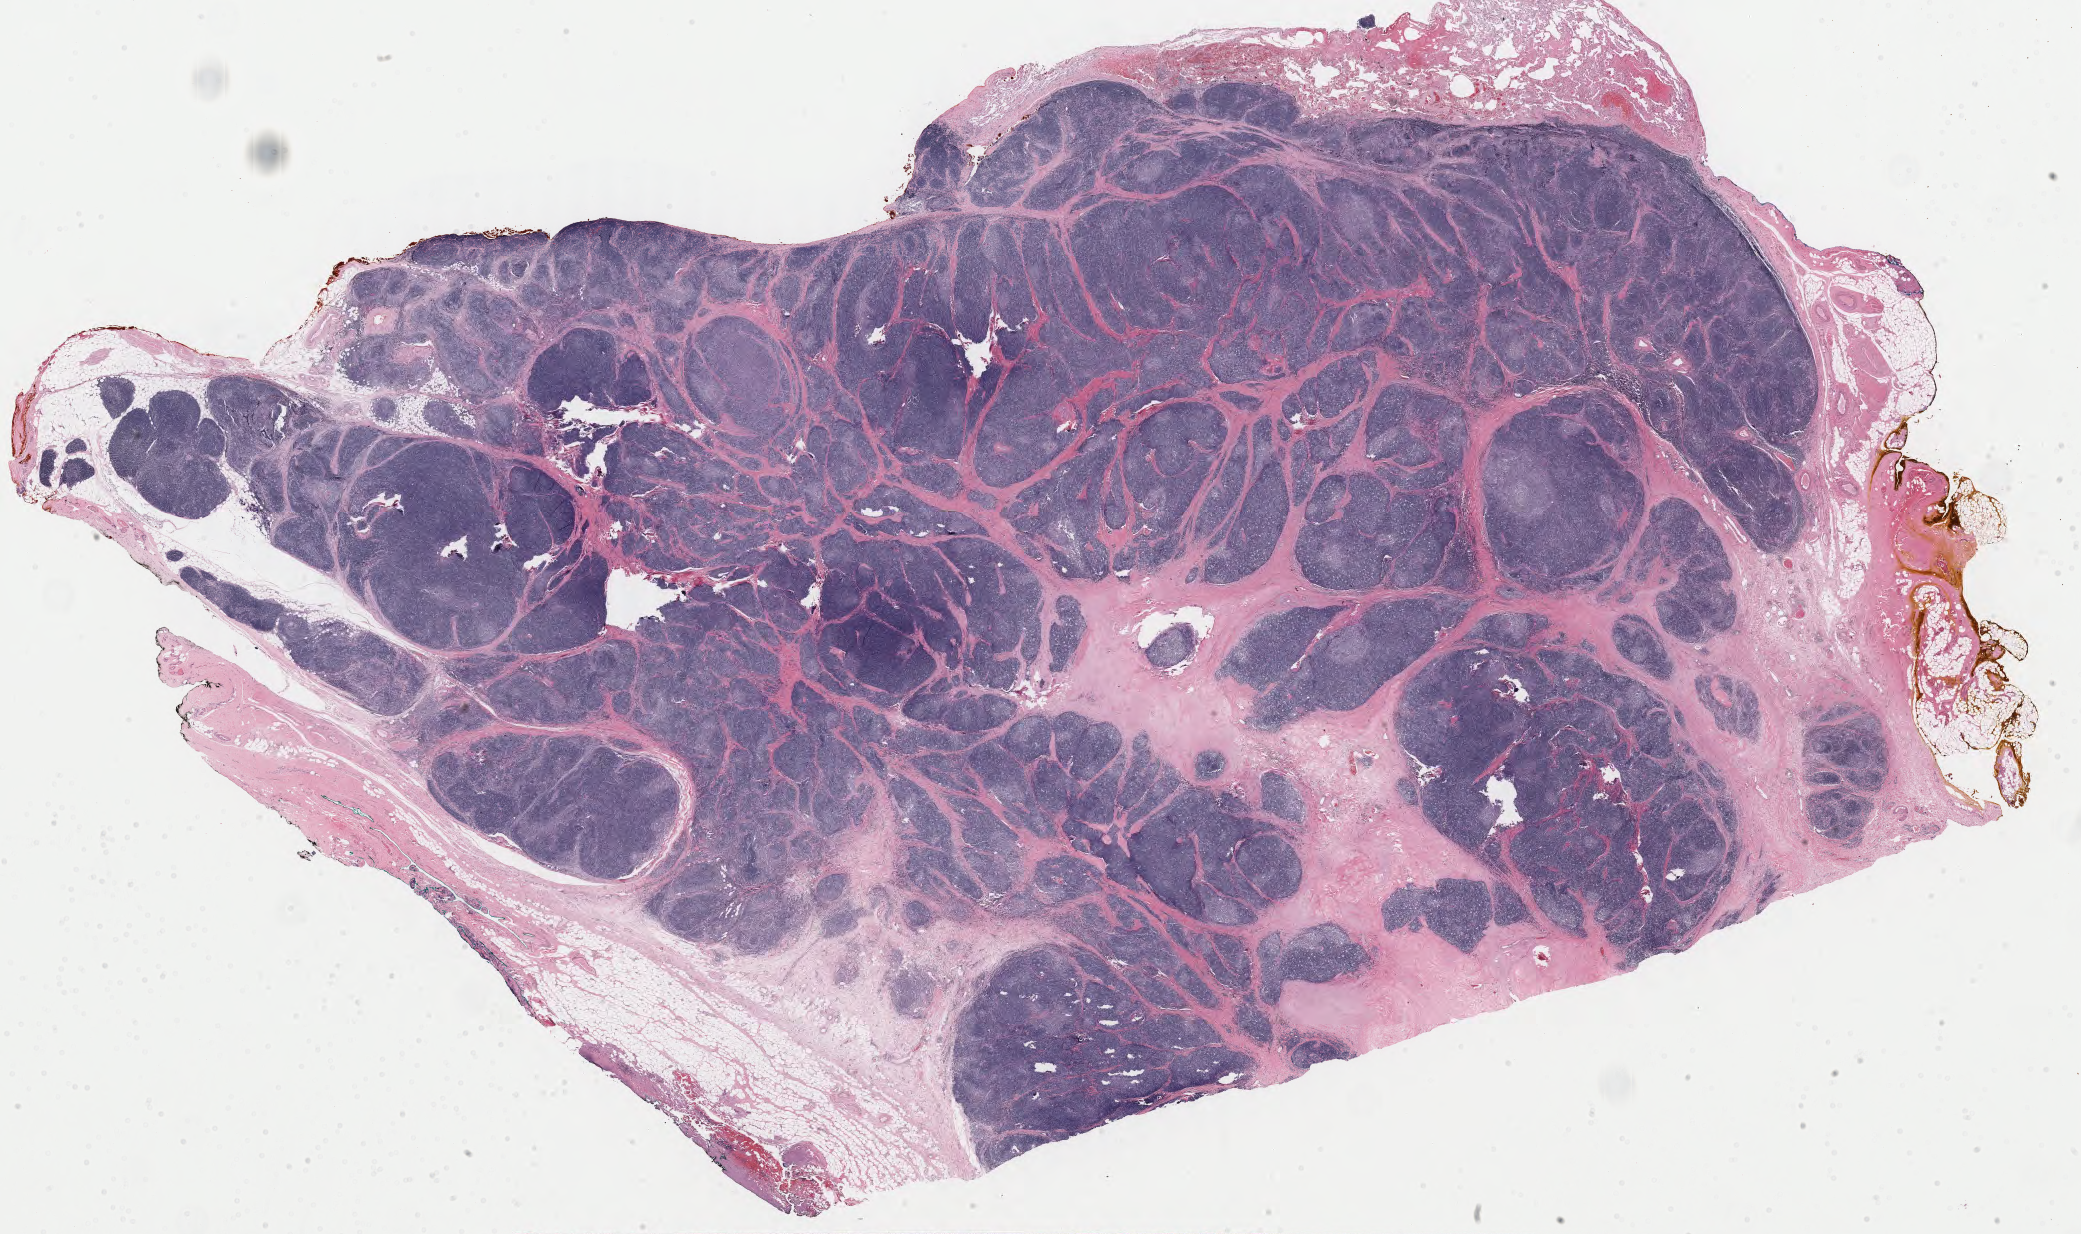
Hematoxylin and eosin (H&E) stained whole-slide image, whole scanned area (about 33.0 x 19.6 mm, slide scanned at 40x) shown as a low-resolution overview. FFPE section. Thymus, primary tumour sample. Patient: female, age at initial diagnosis 57 years.
• pathologic diagnosis: Thymoma, type B1, NOS